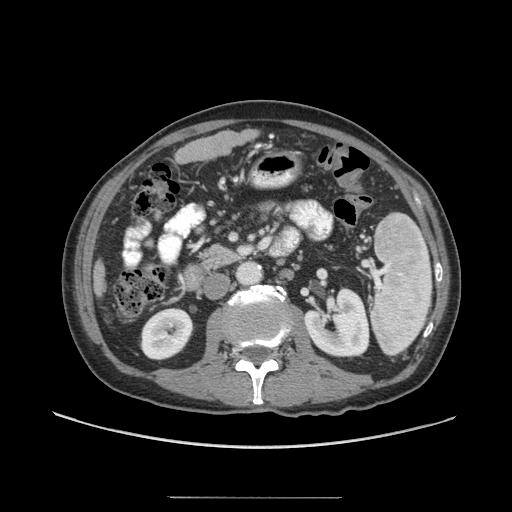
Contrast-enhanced abdominal CT (liver protocol), one axial slice; position 12 of 71 along the scan axis; soft-tissue window (W 400 / L 40 HU); 2.5 mm slice thickness; 512 × 512 image matrix, field of view 400 × 400 mm. Case-level facts recorded for this patient, not image findings: diagnosis: hepatocellular carcinoma (patient treated with transarterial chemoembolisation; whether this scan precedes or follows treatment is not stated here); TNM stage (as recorded): Stage-I; Child-Pugh class: A; tumour differentiation: well differentiated; tumour nodularity: uninodular.
Outlined on this slice (semi-automatically segmented with operator editing):
- liver parenchyma outside the tumour (the mass and vessels are separate outlines, so this box may not span the whole liver): bounding box (x1, y1, x2, y2) in pixels: (94, 130, 256, 296)